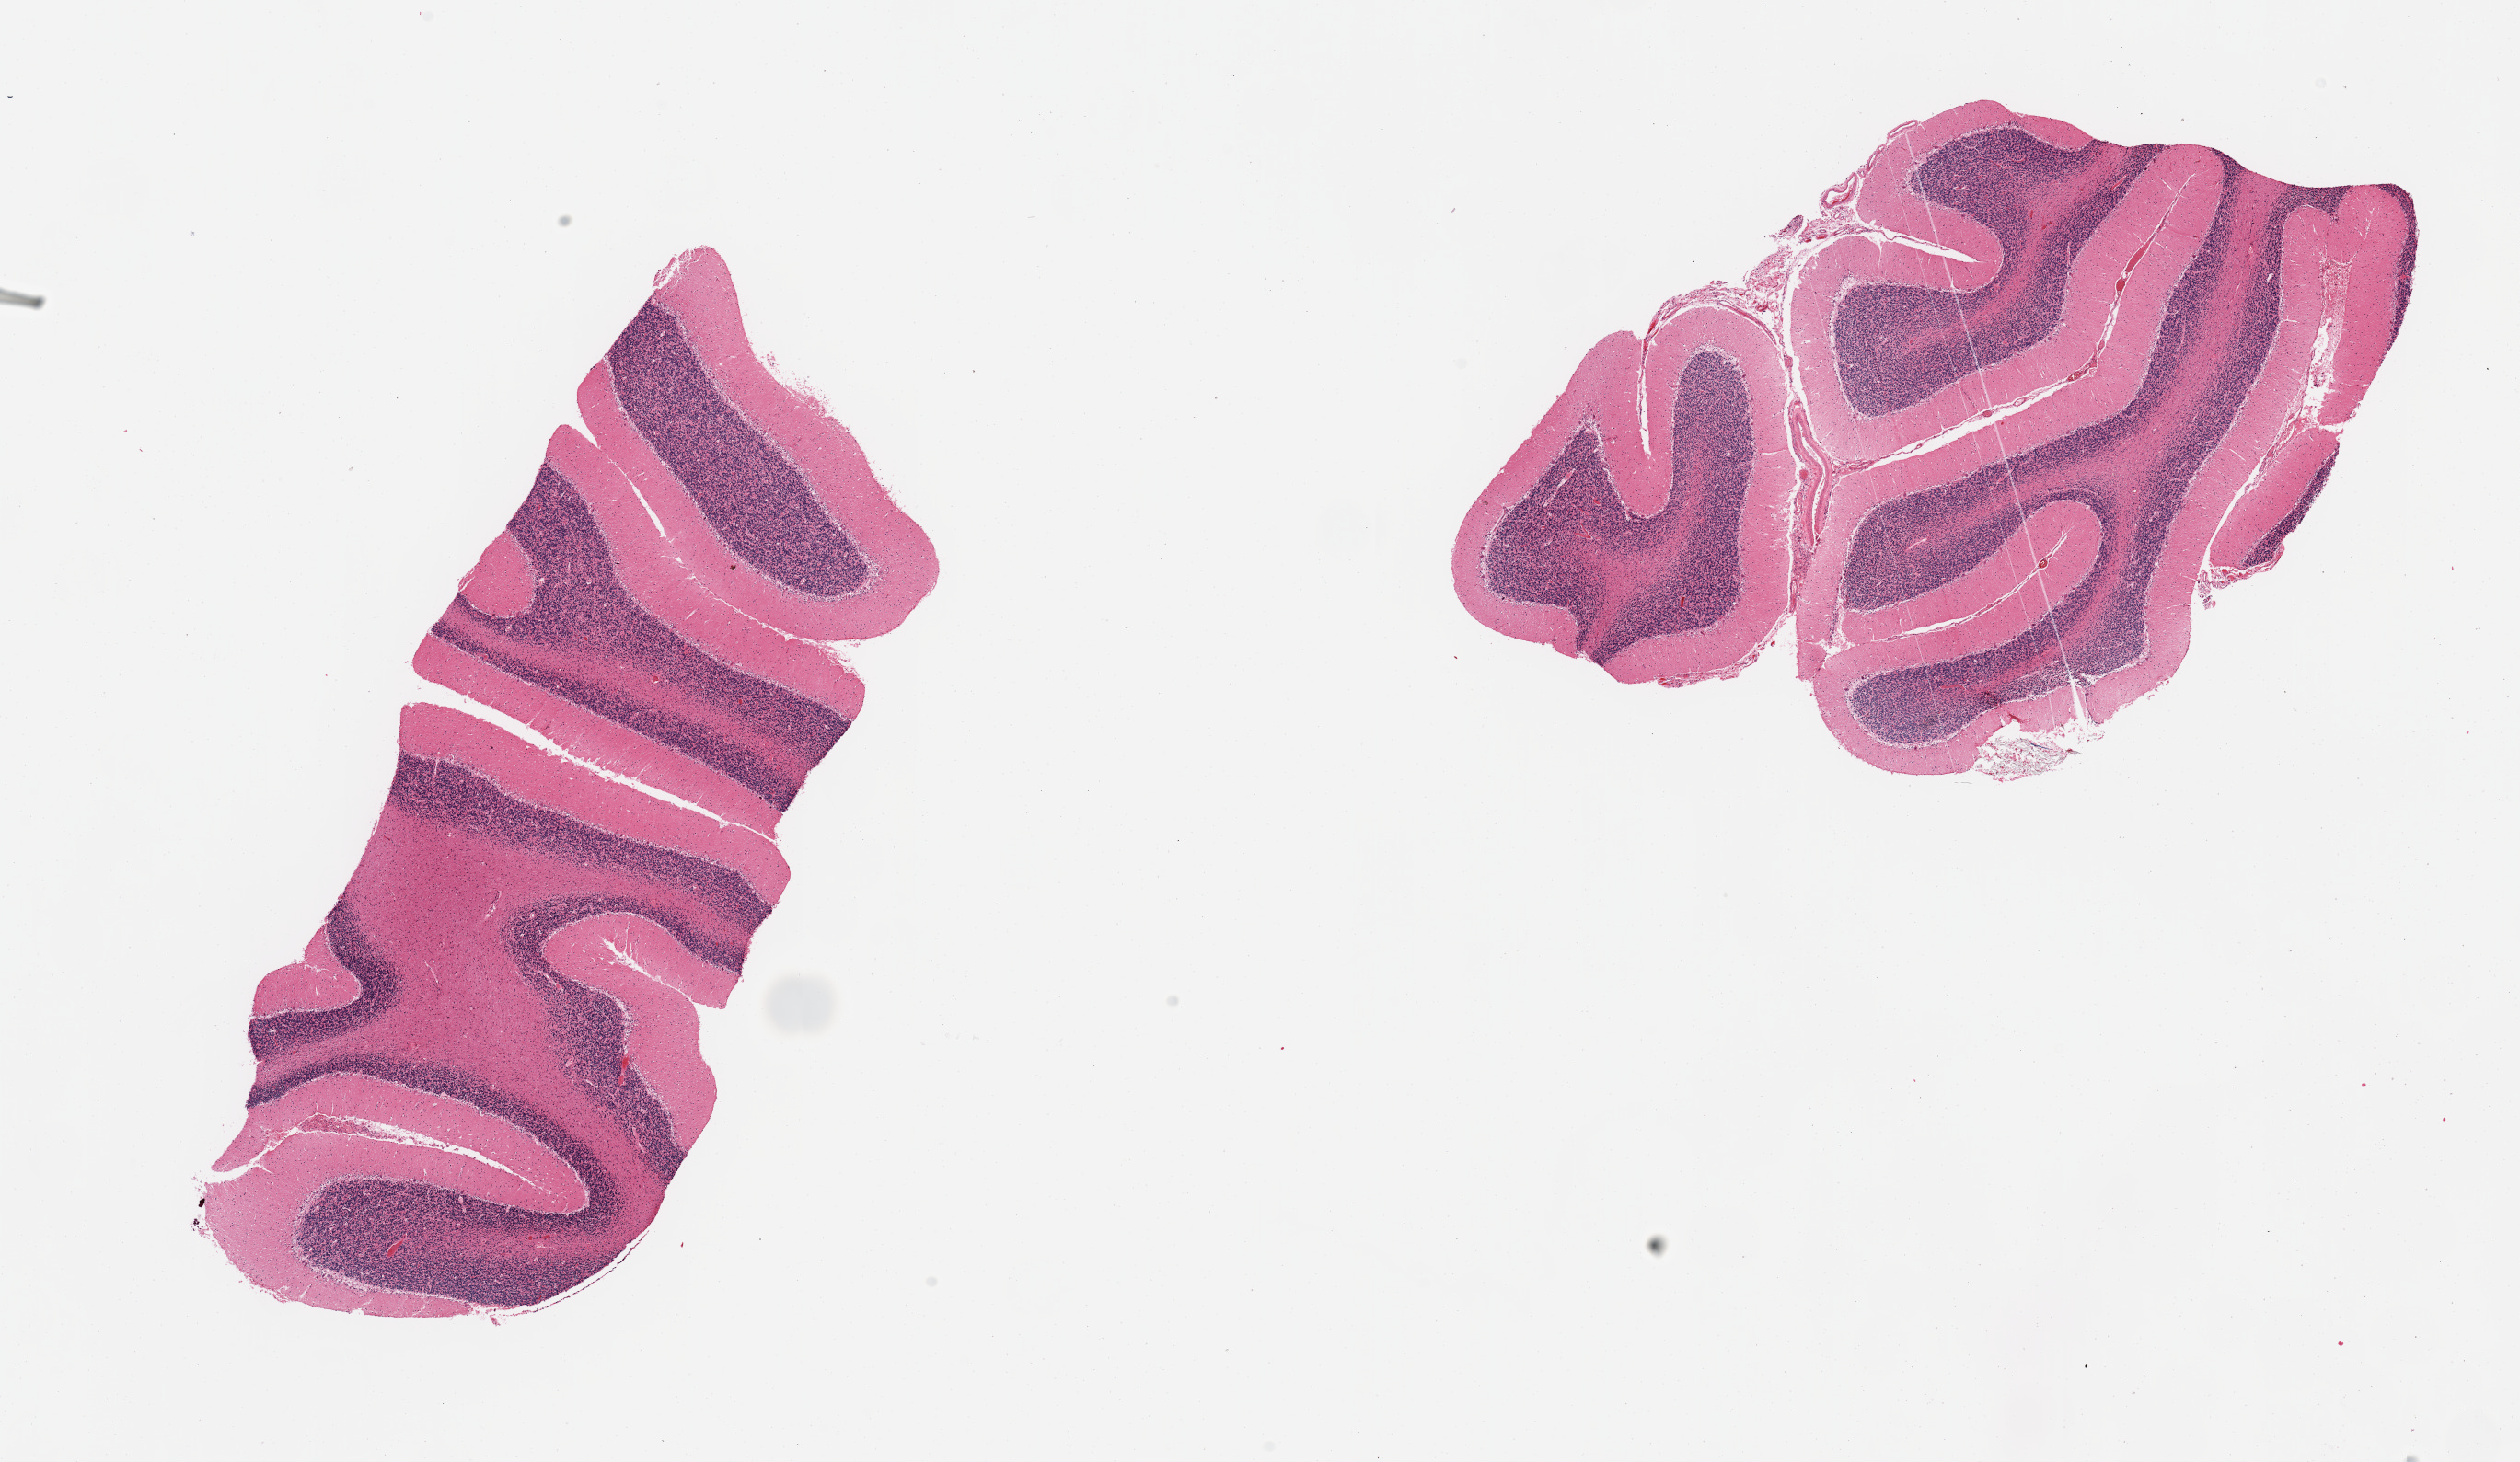
Whole-slide image, hematoxylin and eosin (H&E) stain, a low-resolution overview of the entire scanned area, about 21.7 x 12.6 mm (acquisition: 20x scan), PAXgene-fixed paraffin-embedded (PFPE) section, sampled site (target tissue): cerebellum, donor tissue sample.
Pathologist's review note for this sample: 2 pieces: meninges present in 1.